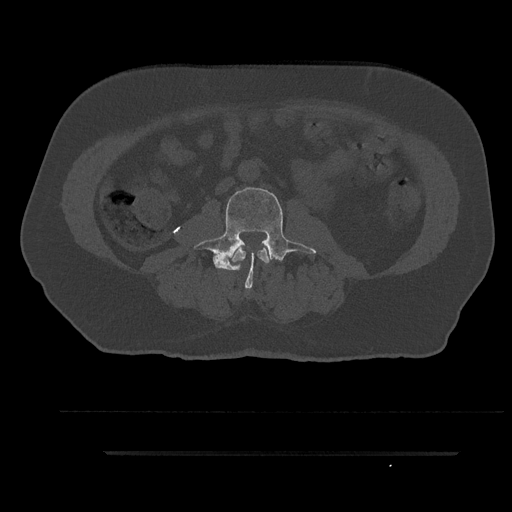
CT including the spine, one axial slice; slice 53 of 797 in the series (ordered by position); reconstruction kernel Br40s/3; bone window (W 1800 / L 400 HU); 0.5 mm slice thickness; 512 × 512 image matrix, field of view 432 × 432 mm. Patient: male, 63 years. From the clinical record (not read from this slice): primary cancer: renal.
Annotated regions visible in this slice (semi-automatic segmentation, software-assisted and operator-edited):
- L2 vertebra: bounding box <232,248,269,271> (left, top, right, bottom; pixels)
- L3 vertebra: <193,185,316,289>